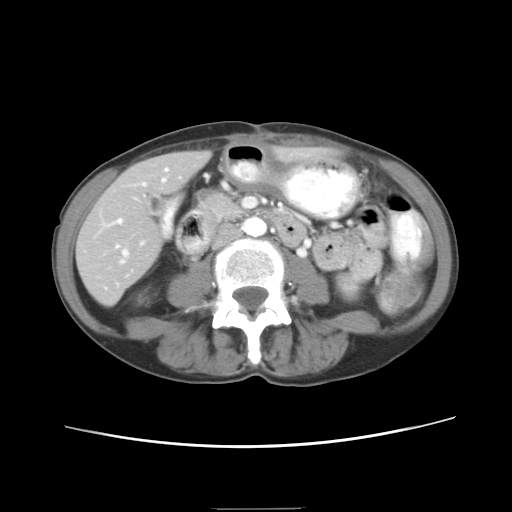
Contrast-enhanced abdominal CT, one axial slice; slice 4 of 26 in the series (ordered by position); intravenous contrast given; soft-tissue window (W 400 / L 40 HU); 7.5 mm slice thickness; 512 × 512 image matrix. Female patient, age 65 years. From the clinical record (not read from this slice): diagnosis: colorectal cancer liver metastases, imaged before liver resection; multiple liver metastases: no.
Structures marked on this image (expert manual segmentation):
- hepatic veins: bounding box <101,168,180,263> (left, top, right, bottom; pixels)
- liver: <78,153,204,304>
- planned liver remnant (the part of the liver to remain after resection): <78,153,204,304>
- portal vein (with intrahepatic branches): <115,244,119,248>